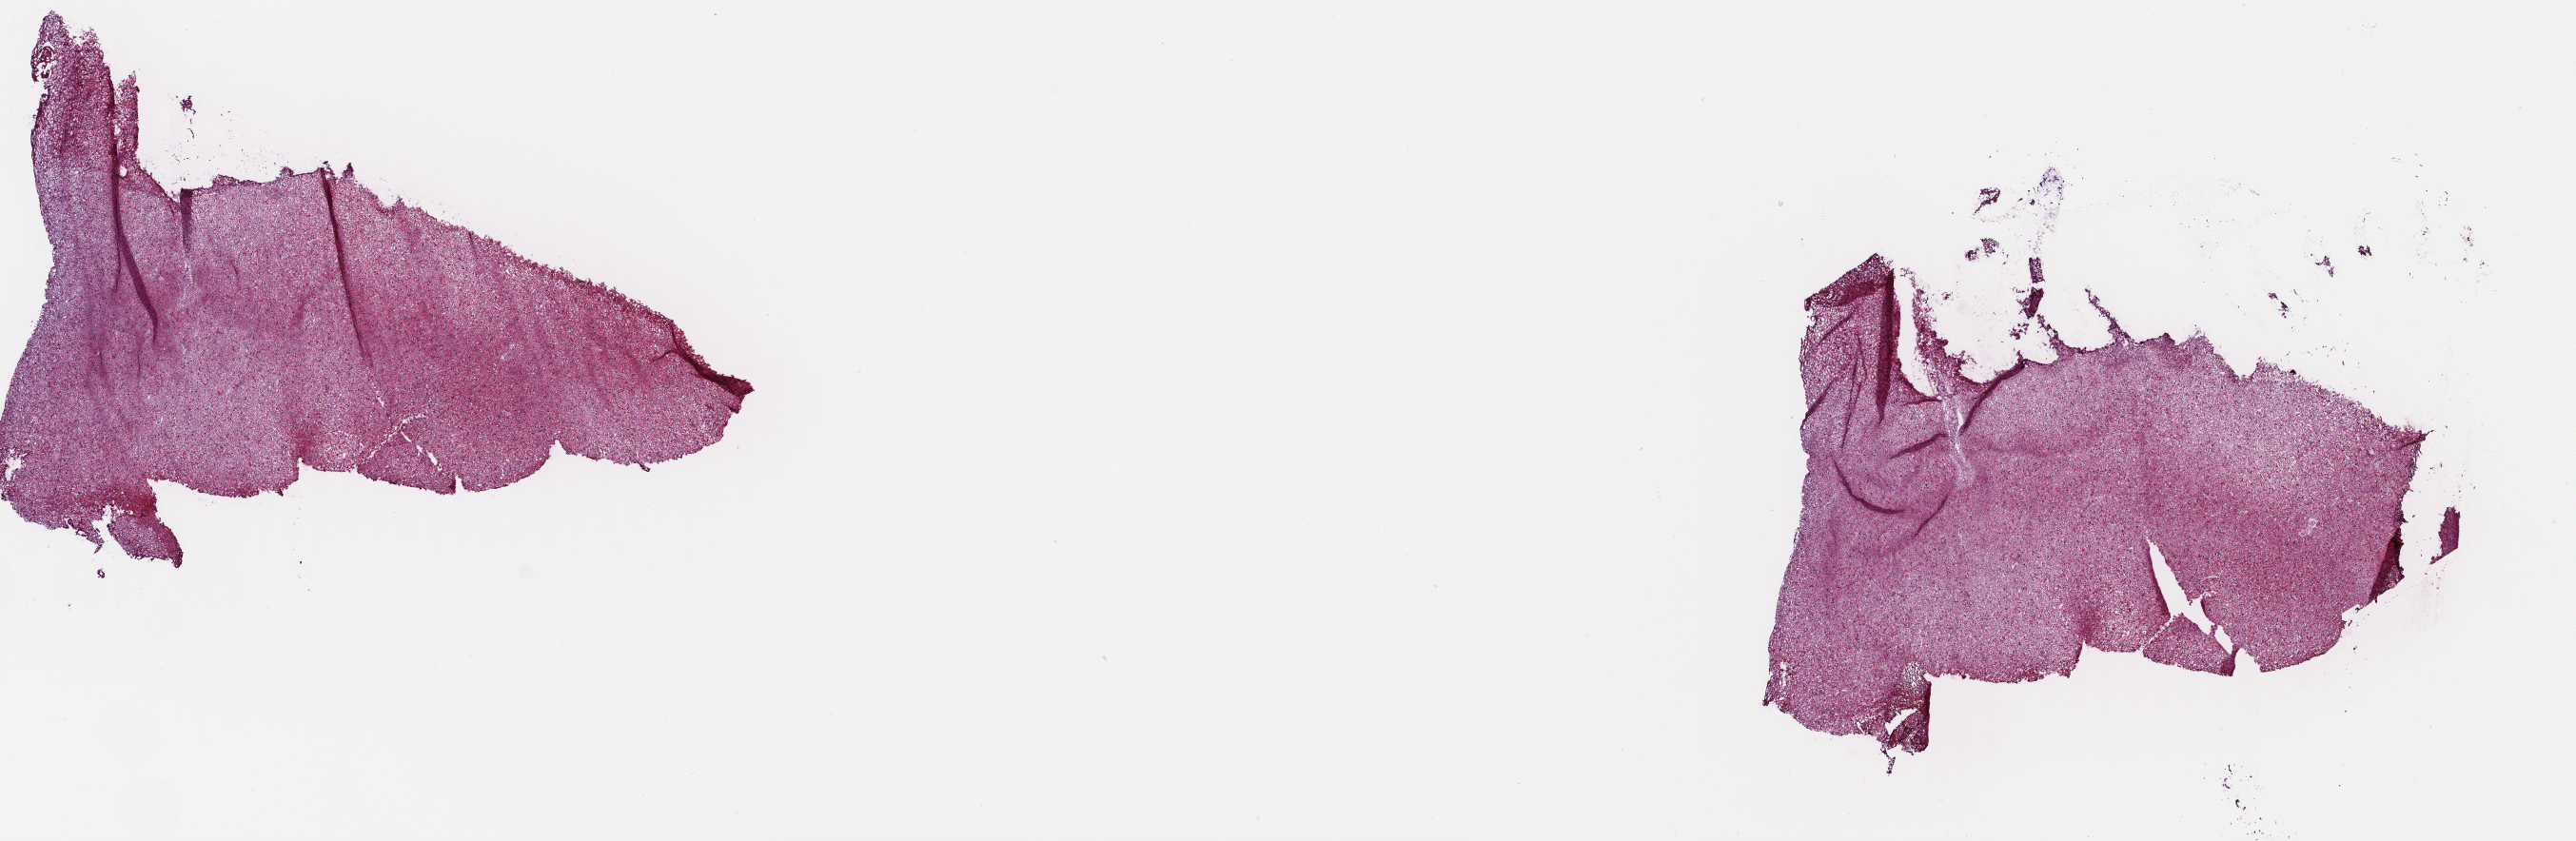
H&E whole-slide image — shown as a low-resolution overview of the whole scanned area (about 21.3 x 6.9 mm, slide scanned at 40x); frozen section from the top of the tissue portion; brain, primary tumour sample. Female, age 38 years at initial diagnosis. Histologic grade: G3 (poorly differentiated). Composition of this section per pathologist review: tumour cells 40%, tumour nuclei 80%, normal cells 10%, stromal cells 50%, necrosis 0%. Inflammatory infiltration, as recorded: lymphocyte infiltration 0%, monocyte infiltration 0%, neutrophil infiltration 0%.
Histologic diagnosis: Astrocytoma, anaplastic.